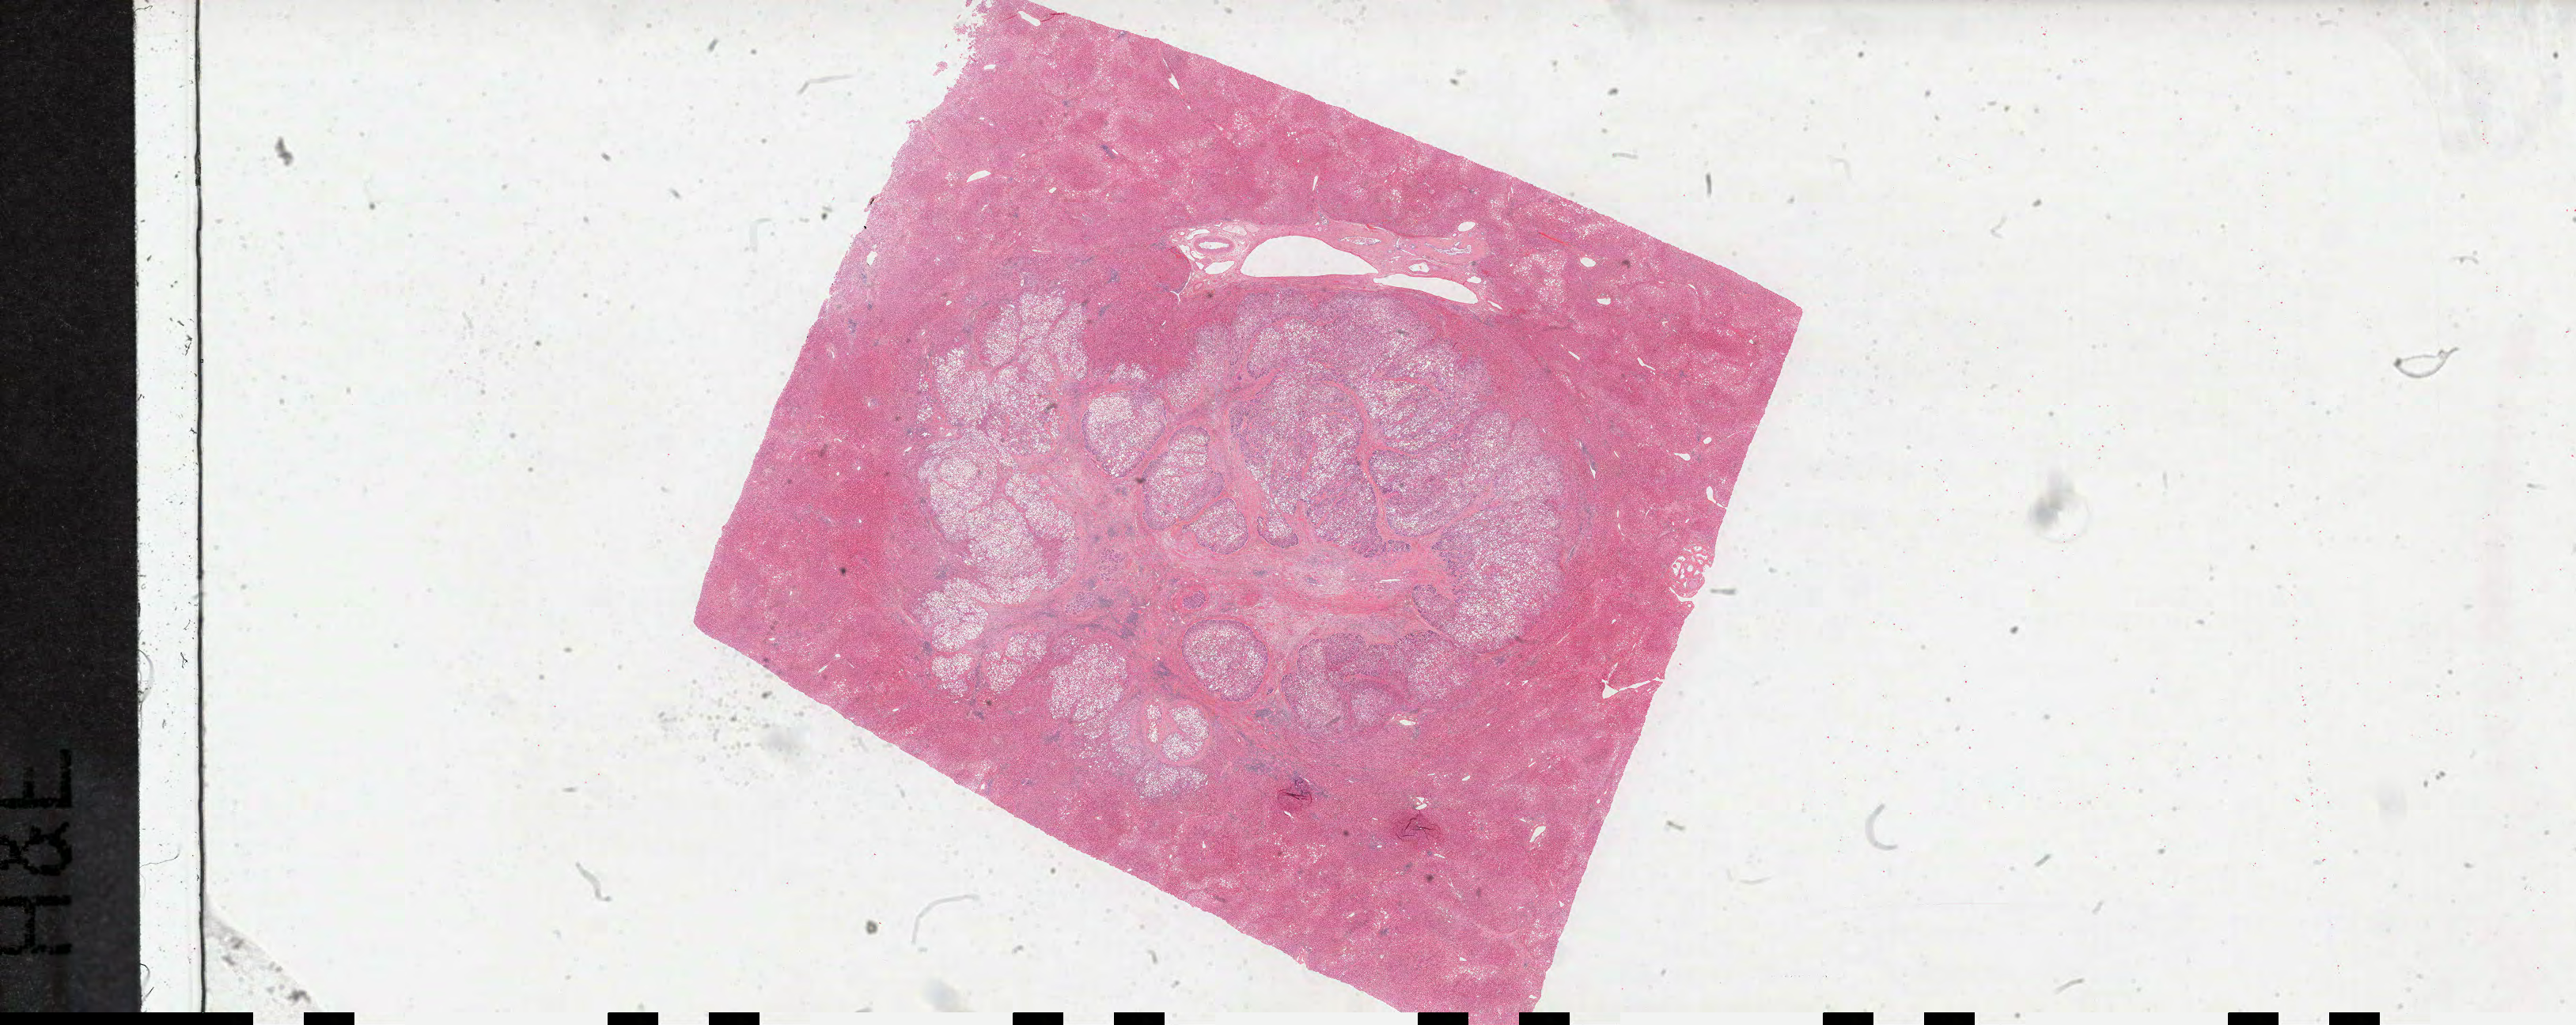
Hematoxylin and eosin (H&E) stained whole-slide image — low-resolution overview of the scanned area, about 52.7 x 21.0 mm (acquisition: 40x scan); formalin-fixed paraffin-embedded (FFPE) diagnostic section; sample: primary tumour, liver. Male, age 73 years at initial diagnosis. Histologic grade: G2 (moderately differentiated).
Histologic diagnosis: Hepatocellular carcinoma, NOS. AJCC pathologic stage: II (7th edition).